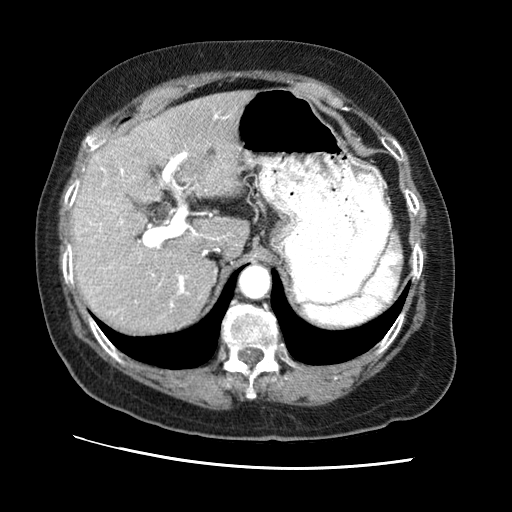
Contrast-enhanced abdominal CT (liver protocol), one axial slice. Slice 45 of 65 in the series (ordered by position). 120 kVp. Soft-tissue window (W 400 / L 40 HU). 512 × 512 image matrix. Case-level facts recorded for this patient, not image findings: diagnosis: hepatocellular carcinoma (patient treated with transarterial chemoembolisation; whether this scan precedes or follows treatment is not stated here); TNM stage (as recorded): Stage-II; Child-Pugh class: A; tumour differentiation: no biopsy; tumour nodularity: multinodular.
Structures marked on this image (semi-automatically segmented with operator editing):
- liver parenchyma outside the tumour (the mass and vessels are separate outlines, so this box may not span the whole liver): bounding box <72,90,252,332> (left, top, right, bottom; pixels)
- liver vessels: <101,114,227,307>